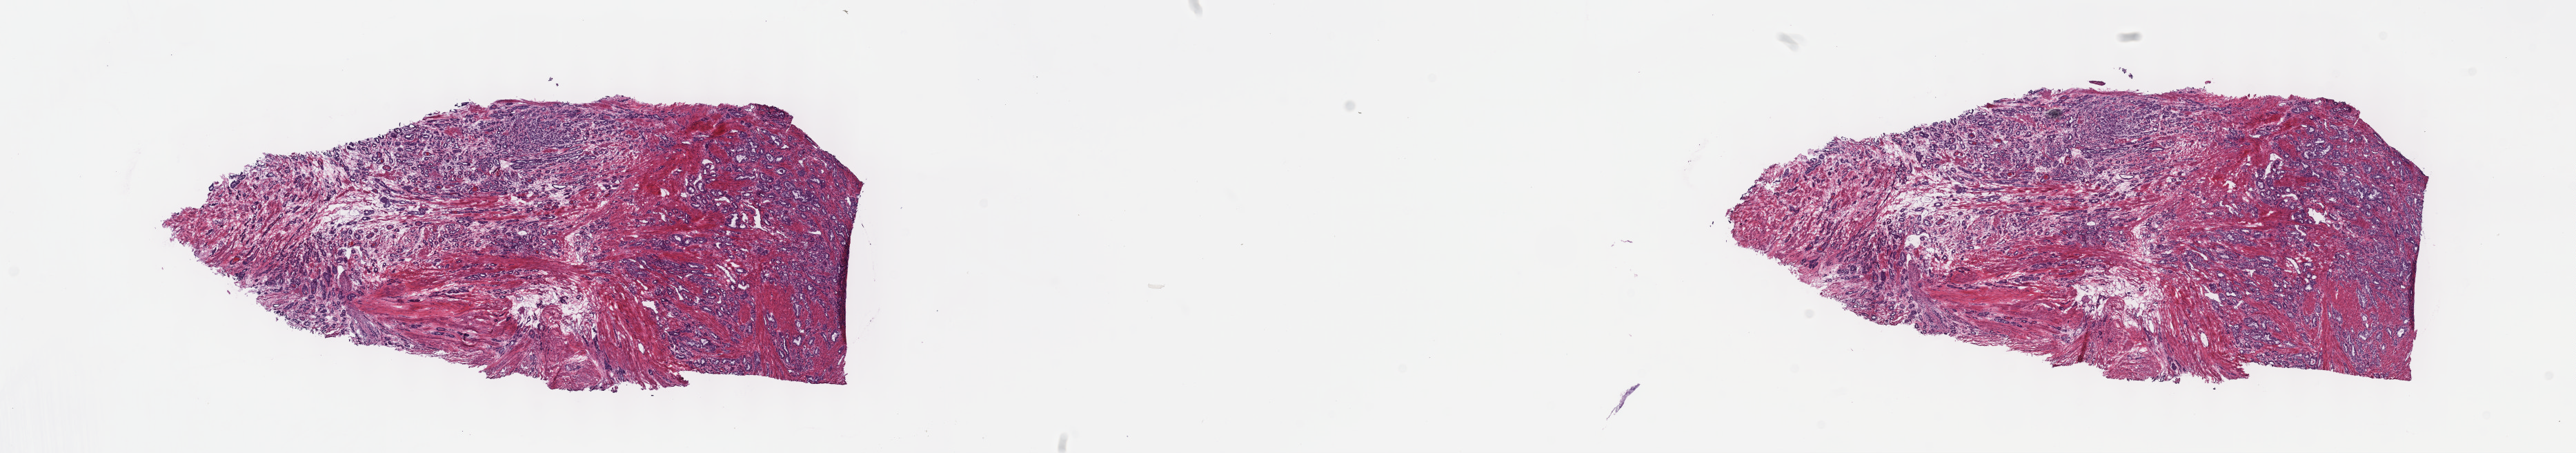
Digitized H&E tissue section (whole slide), whole scanned area (about 30.2 x 5.3 mm, from a 40x scan) shown as a low-resolution overview. Frozen section from the top of the tissue portion. Primary tumour sample from the prostate. Patient: male, age at initial diagnosis 51 years.
Pathologic diagnosis: Adenocarcinoma, NOS (prostate gland).